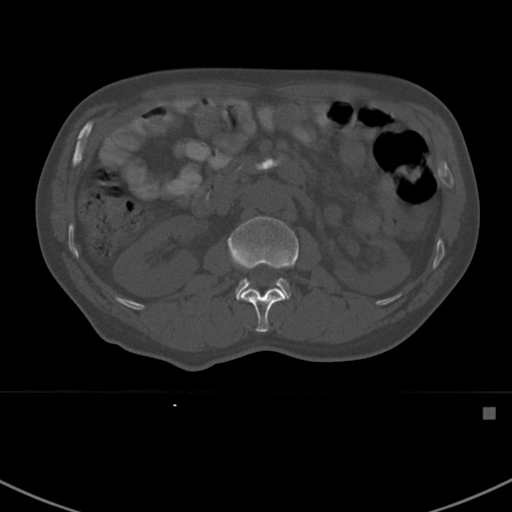
CT including the spine, one axial slice; slice 298 of 412 in the series (ordered by position); reconstruction kernel Br40s; bone window (W 1800 / L 400 HU); 512 × 512 image matrix, field of view 358 × 358 mm. Patient: male, 59 years. From the clinical record (not read from this slice): primary cancer: prostate.
Outlined on this slice (semi-automatic segmentation, software-assisted and operator-edited):
- L1 vertebra: bounding box (x1, y1, x2, y2) in pixels: (240, 287, 286, 333)
- L2 vertebra: (227, 216, 299, 301)